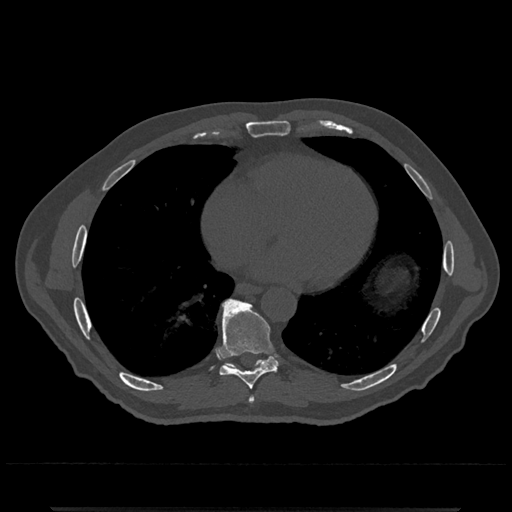
CT including the spine, one axial slice. Slice 657 of 797 in the series (ordered by position). Reconstruction kernel Br40s/3. Bone window (W 1800 / L 400 HU). 0.5 mm slice thickness. 512 × 512 image matrix, field of view 393 × 393 mm. Patient: male, 67 years. From the clinical record (not read from this slice): primary cancer: prostate.
Structures marked on this image (semi-automatic segmentation, software-assisted and operator-edited):
- T7 vertebra: box from (x=248, y=396) to (x=254, y=403) px
- T8 vertebra: (x=217, y=298)–(x=281, y=390)
- T9 vertebra: (x=219, y=299)–(x=280, y=369)